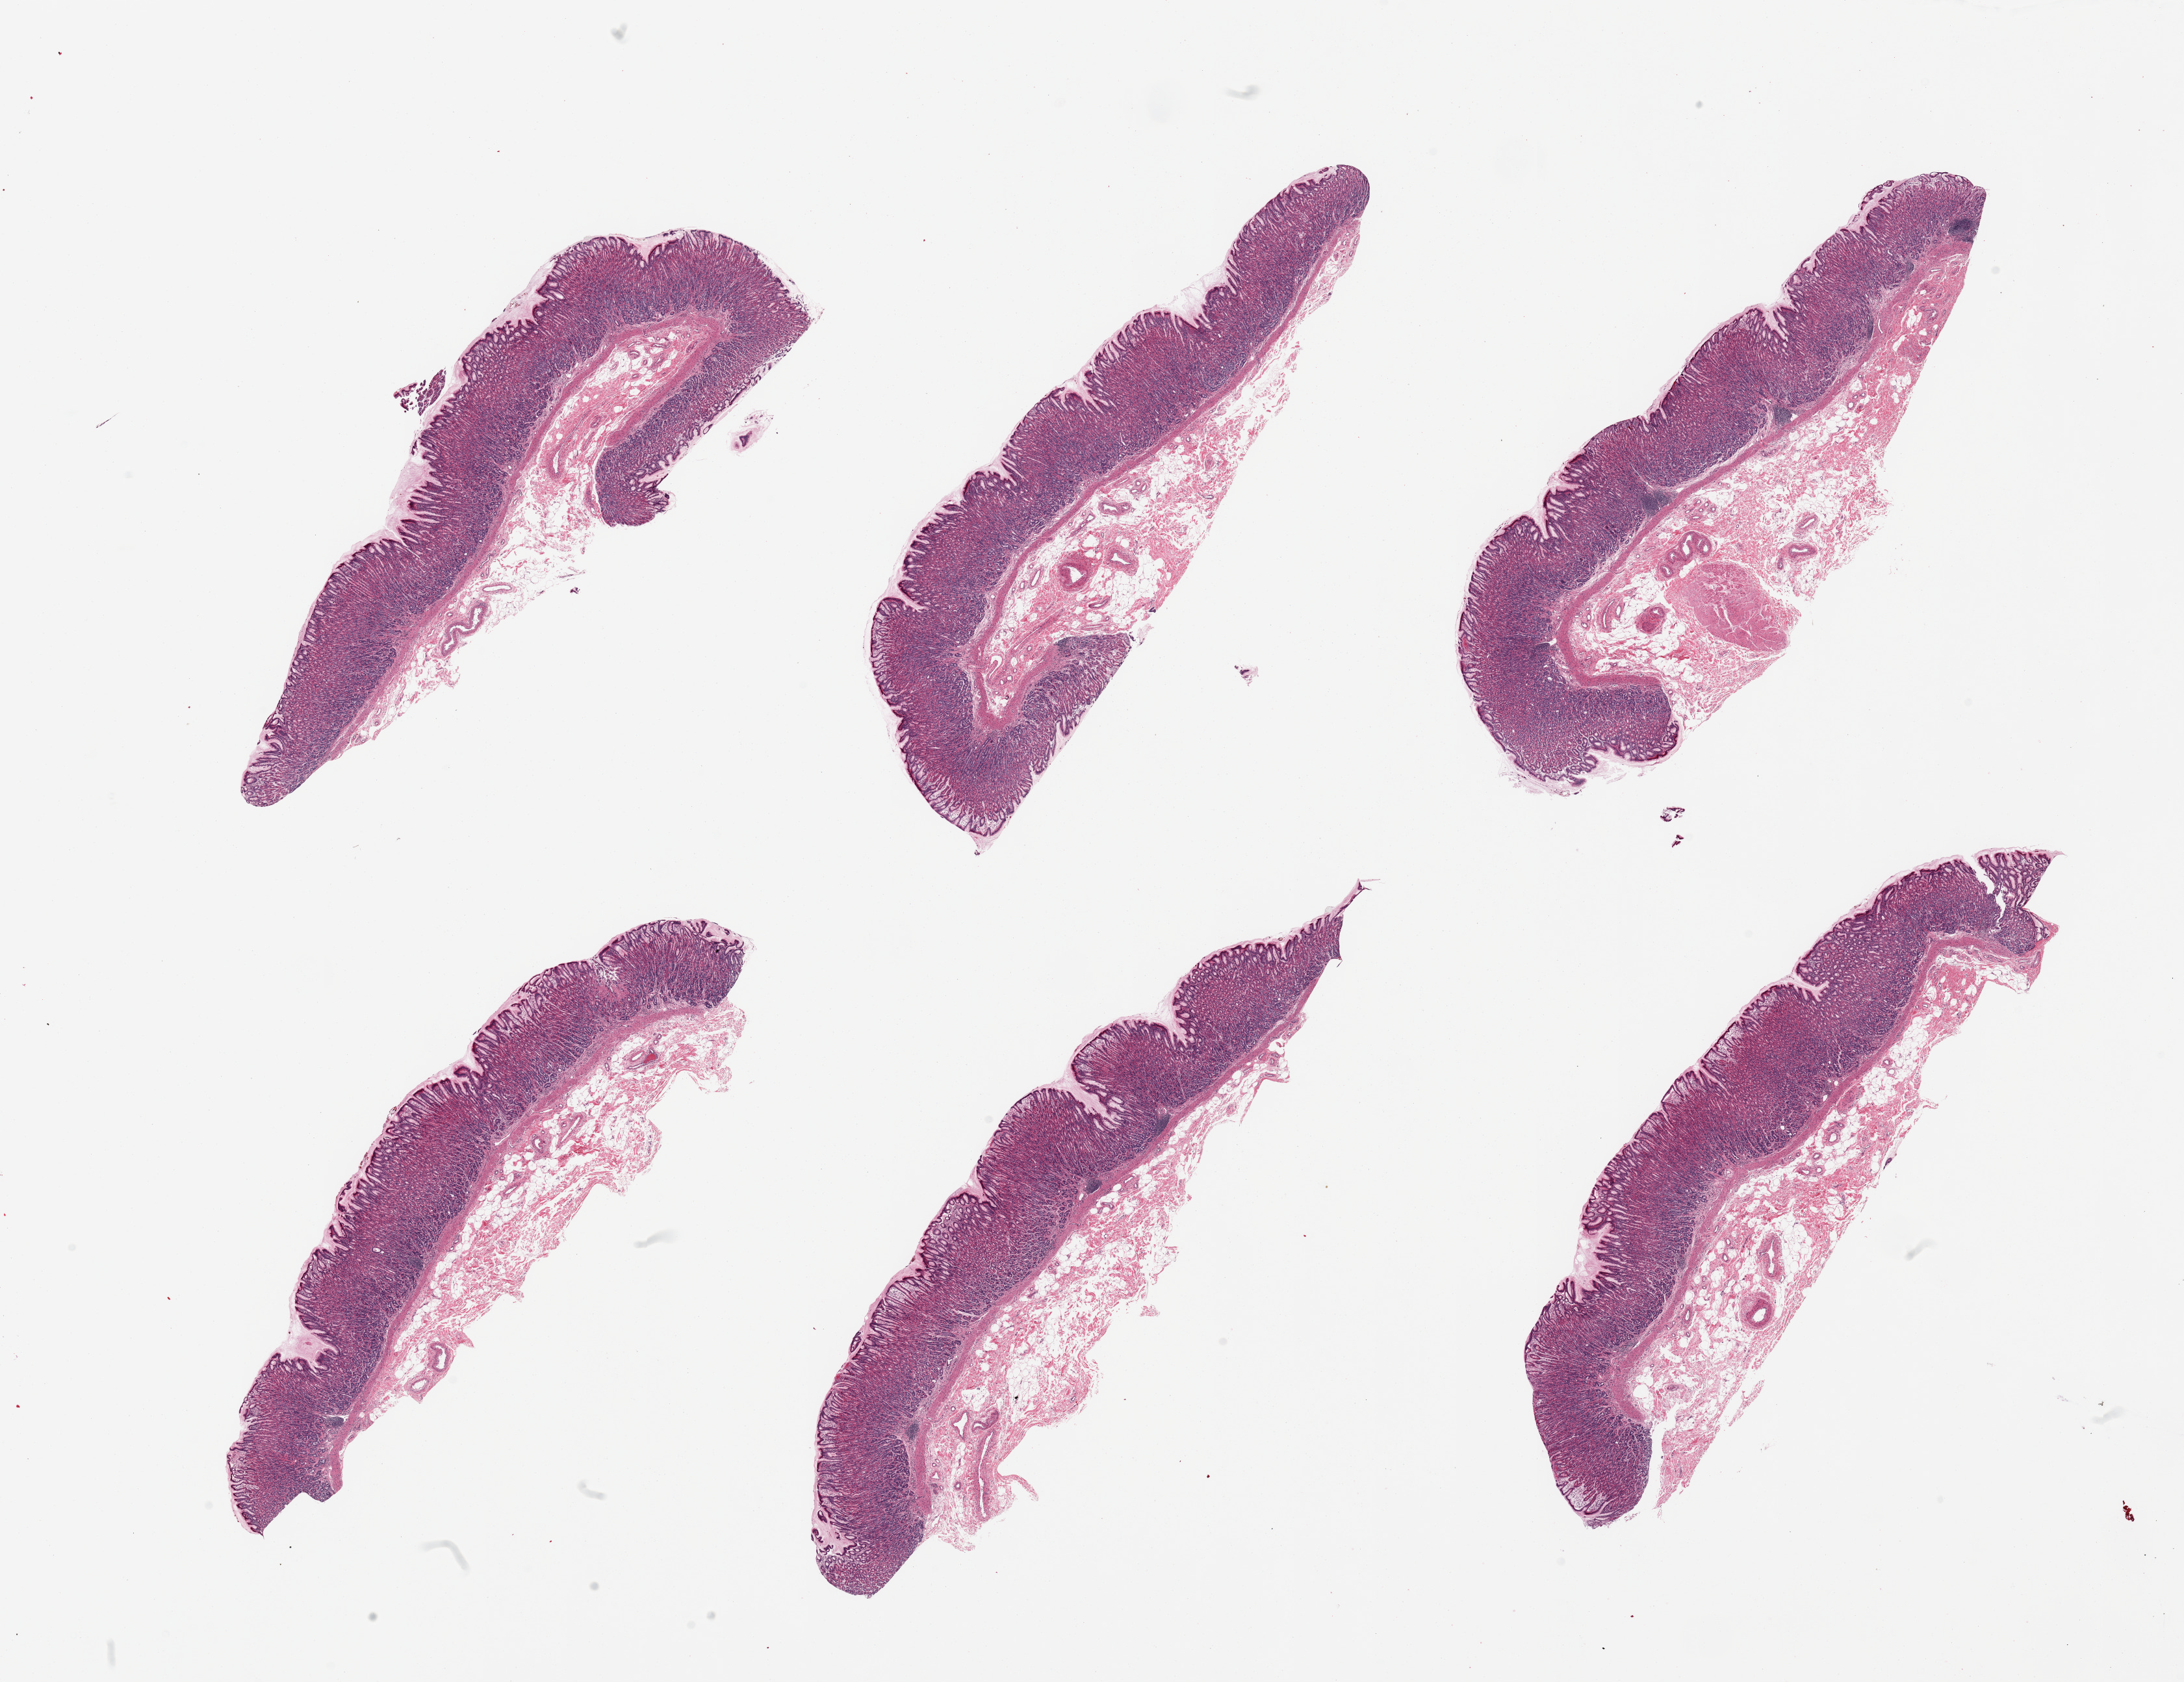
H&E whole-slide image — whole scanned area (about 26.6 x 20.5 mm) shown as a low-resolution overview. PAXgene-fixed, paraffin-embedded tissue. Target tissue: stomach. Donor tissue sample. Donor: female.
Pathologist's review note for this sample: 6 pieces, mucosa extremely well preserved, ~1.2mm, ~50-75% thickness, valuable specimen.